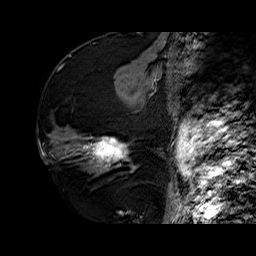
Breast MRI (dynamic contrast-enhanced), one sagittal slice. Position 28 of 60 along the scan axis. Dynamic contrast-enhanced series, time point 2 of 6 at this slice position (early post-contrast). 1.5 T. TE 6.4 ms, TR 32.7 ms. 256 × 256 image matrix, field of view 200 × 200 mm. Female patient. From the clinical record (not read from this slice): setting: breast cancer imaged before/during neoadjuvant chemotherapy; receptor status: HR-positive, HER2-negative.
Annotated regions visible in this slice (semi-automatic segmentation, software-assisted and operator-edited):
- analysis volume of interest (the breast-tissue region the enhancement analysis was run in; not a lesion): bounding box <73,110,140,176> (left, top, right, bottom; pixels)
- tumour enhancement mask (voxels above the 100 % enhancement threshold inside the analysis volume of interest): <84,137,129,166>